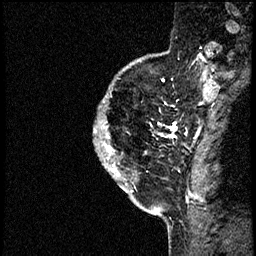
Breast MRI (dynamic contrast-enhanced), one sagittal slice; dynamic contrast-enhanced study with each time point stored as its own series, time point 2 of 4 at this slice position (early post-contrast, ordered by acquisition time); 1.5 T; TE 4.2 ms, TR 17.6 ms; 2 mm slice thickness; 256 × 256 image matrix, field of view 200 × 200 mm. Female patient, age 40 years. From the clinical record (not read from this slice): setting: breast cancer imaged before/during neoadjuvant chemotherapy; receptor status: HER2-positive.
Structures marked on this image (semi-automatically segmented with operator editing):
- analysis volume of interest (the breast-tissue region the enhancement analysis was run in; not a lesion): bounding box [x1, y1, x2, y2] px = [95, 56, 197, 205]
- tumour enhancement mask (voxels above the 100 % enhancement threshold inside the analysis volume of interest): [95, 121, 197, 199]